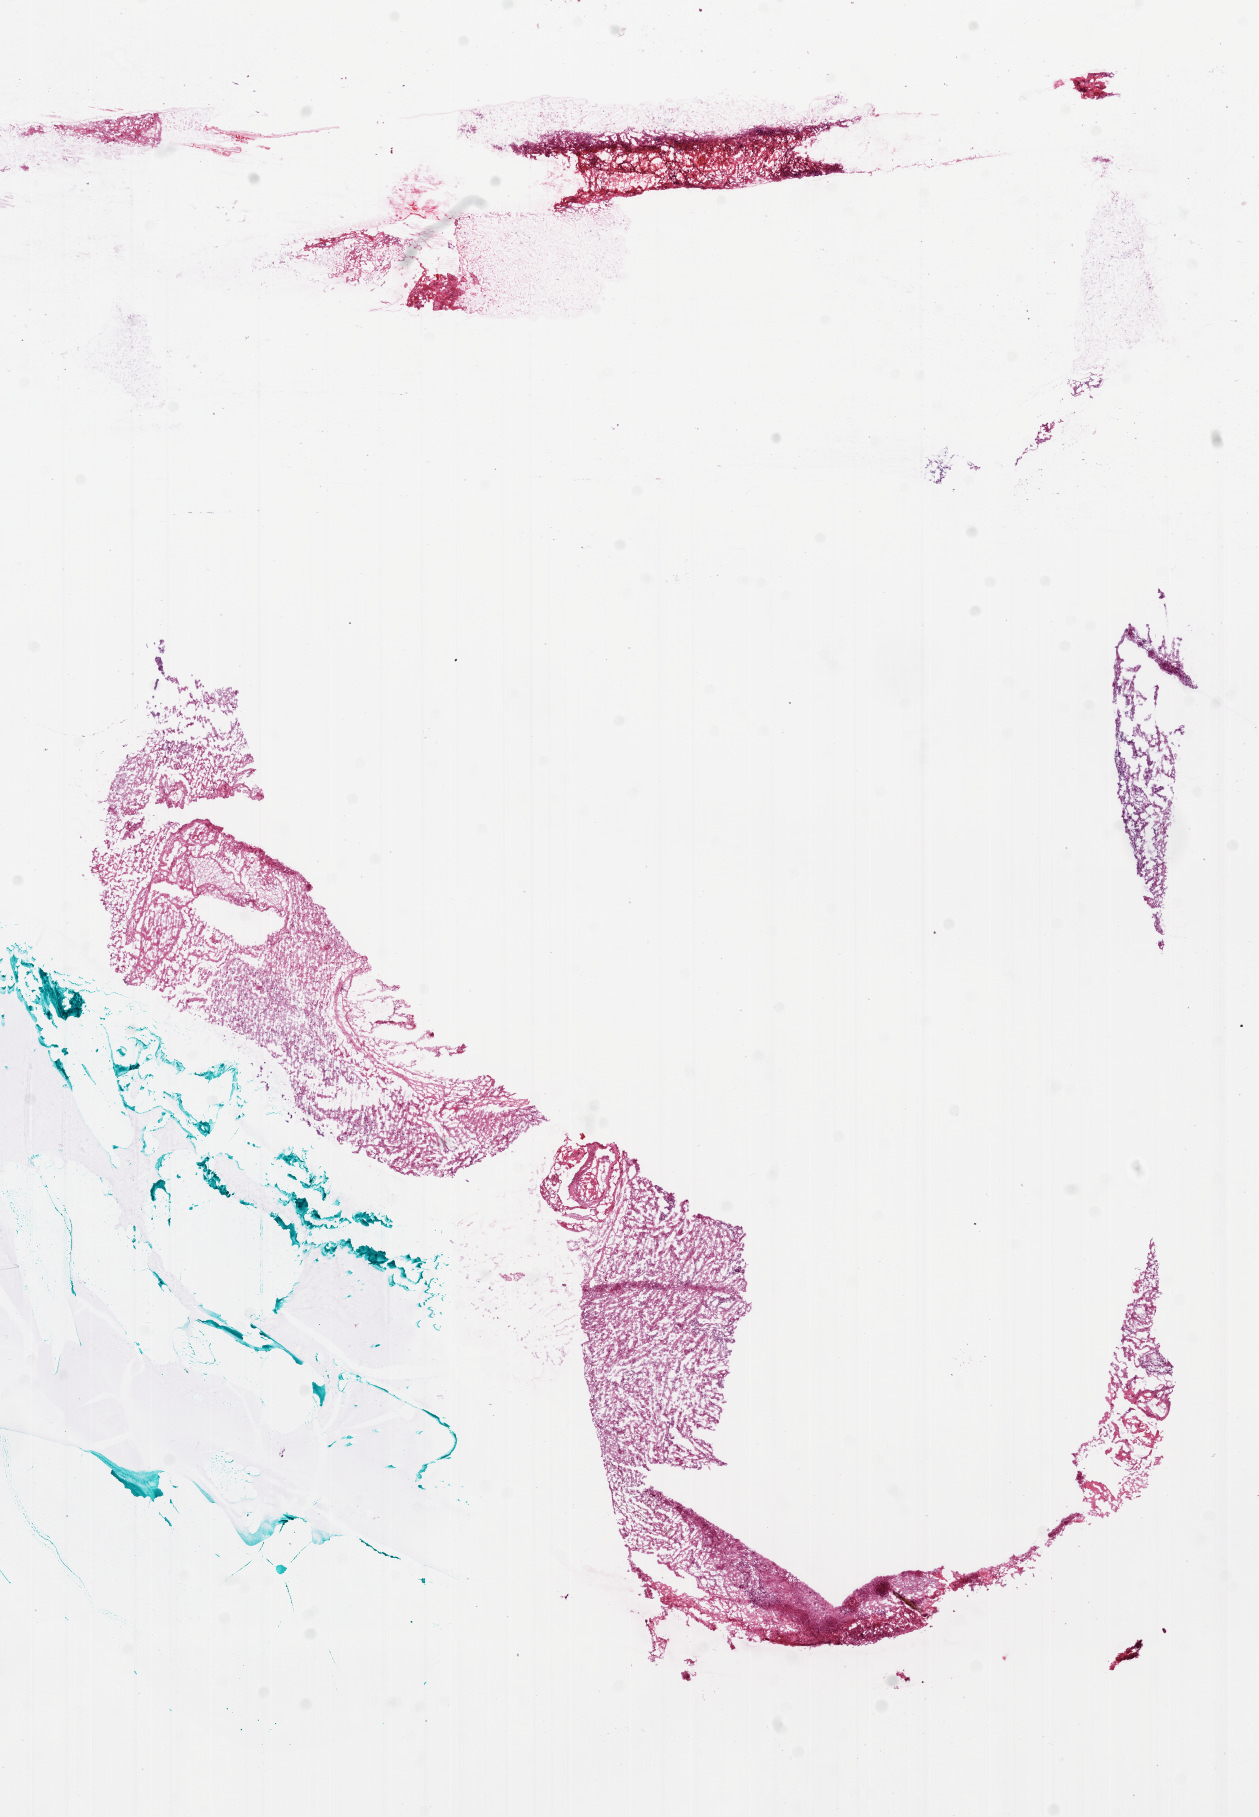
Digitized H&E tissue section (whole slide) — a low-resolution overview of the entire scanned area, about 10.2 x 14.7 mm (acquisition: 20x scan); frozen section; primary tumour sample from the brain. Female patient; age at initial diagnosis 75 years. Pathologist review of this section (percent, as recorded): tumour cells 80%, tumour nuclei 100%, normal cells 0%, stromal cells 0%, necrosis 20%.
Diagnosis: Glioblastoma.